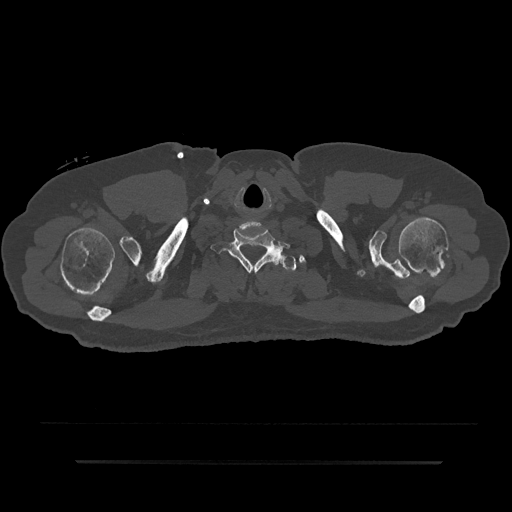
CT including the spine, one axial slice; position 768 of 797 along the scan axis; 120 kVp; bone window (W 1800 / L 400 HU); 0.5 mm slice thickness; 512 × 512 image matrix, field of view 464 × 464 mm. Male patient, age 59 years. From the clinical record (not read from this slice): primary cancer: bile ducts.
Outlined on this slice (semi-automatically segmented with operator editing):
- T1 vertebra: box from (x=271, y=248) to (x=305, y=271) px